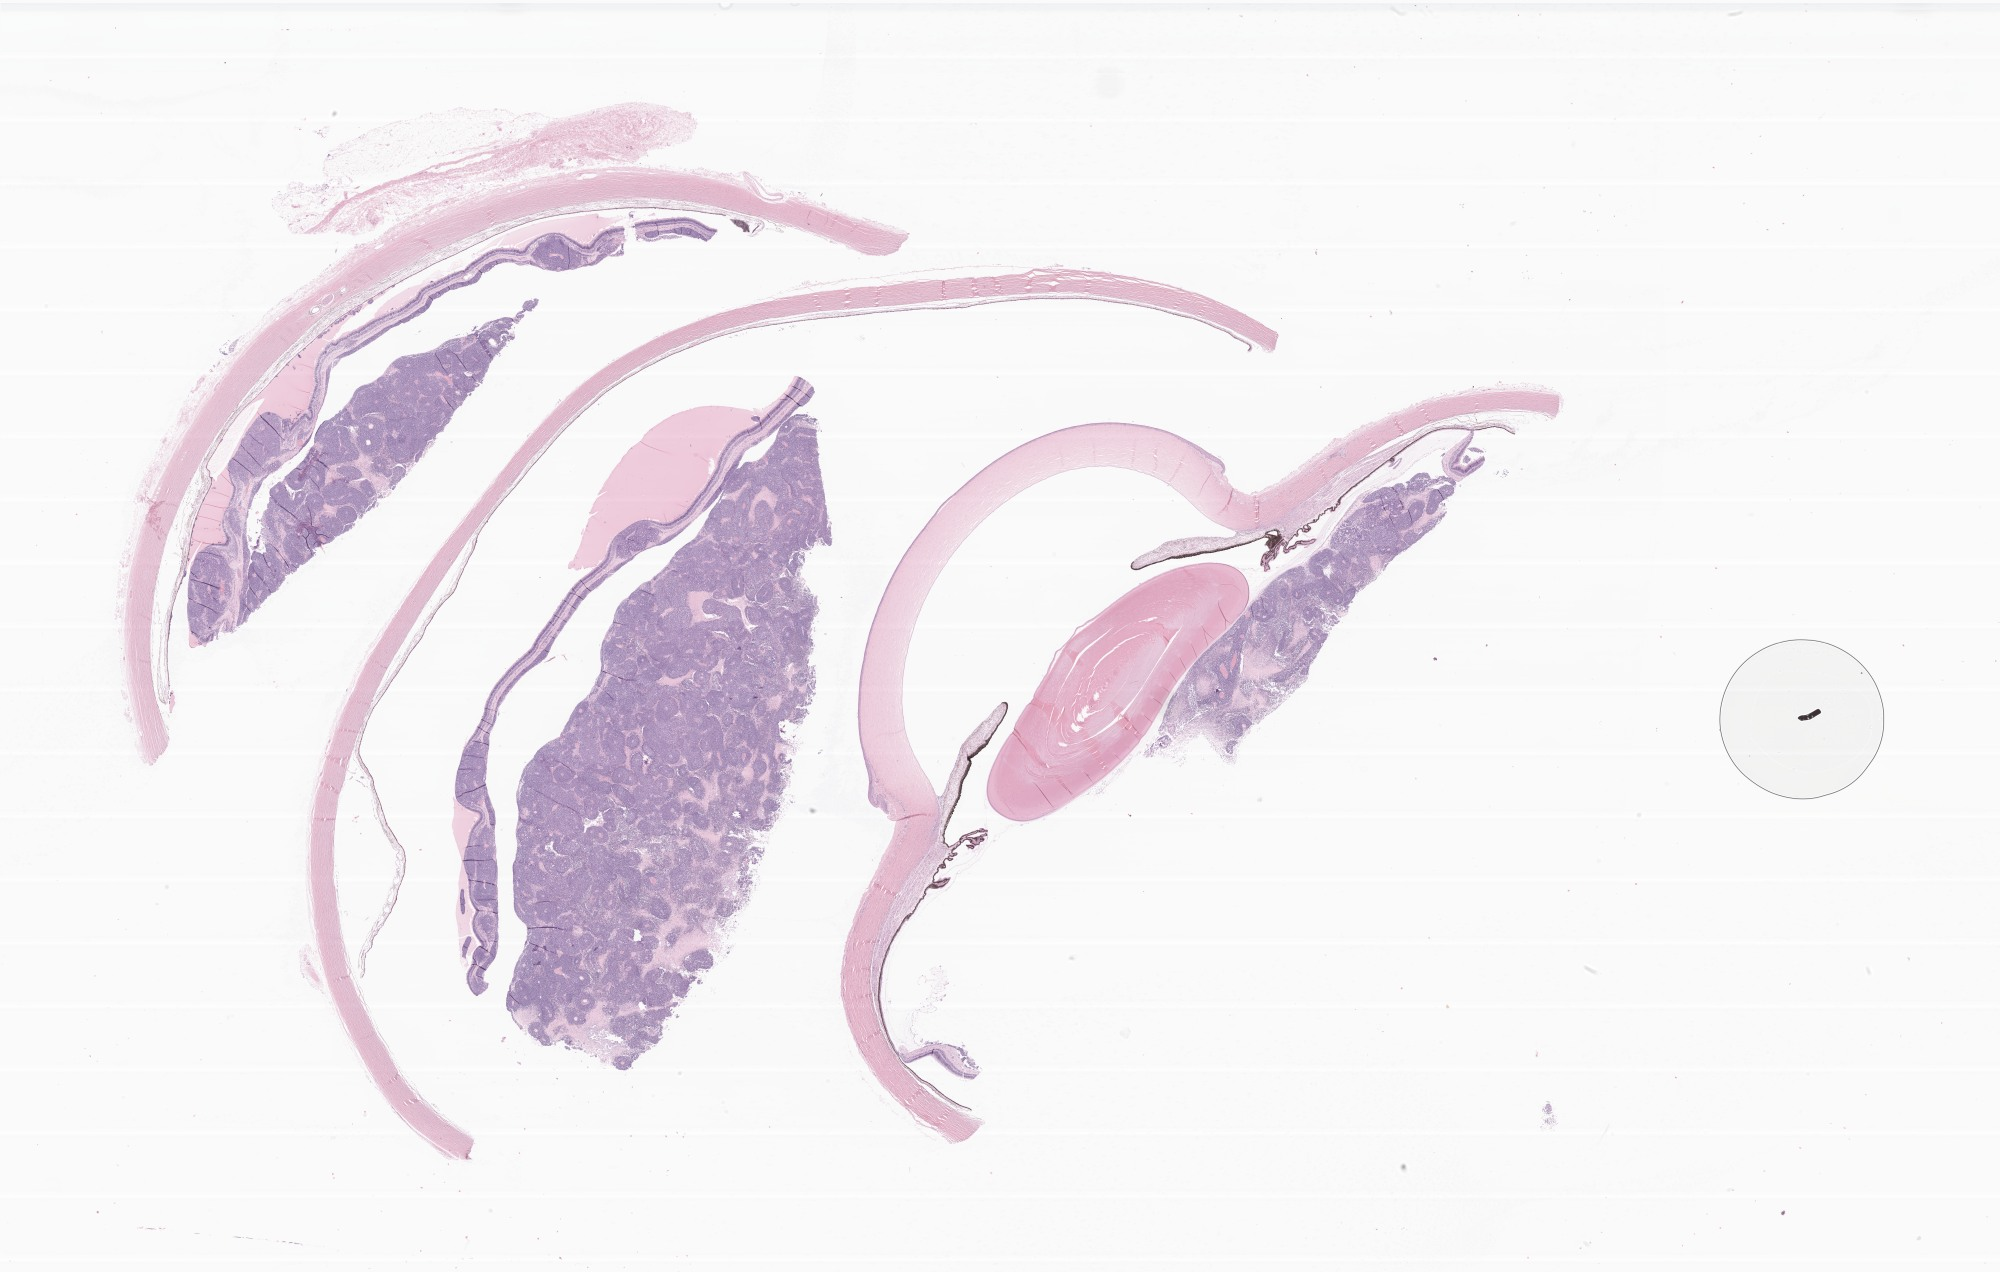
Digitized H&E-stained section of tumor tissue from the retina — whole scanned area (about 33.7 x 21.5 mm) shown as a low-resolution overview; formalin-fixed, paraffin-embedded (FFPE) tissue. Patient male; age 322 days.
* diagnosis (ICD-O-3 morphology term): Retinoblastoma, NOS